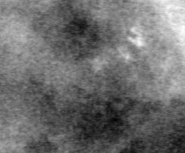
Cropped region of a digitized screen-film mammogram centred on a radiologist-marked abnormality; right breast; MLO view; BI-RADS breast density category 2 (scale 1–4).
- Finding: calcifications, morphology pleomorphic, distribution clustered; BI-RADS assessment category 4; pathology (as recorded): benign.